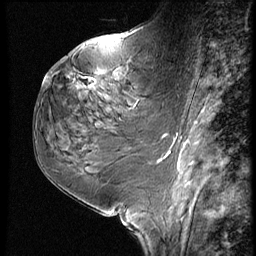
Breast MRI (dynamic contrast-enhanced), one sagittal slice. Position 30 of 60 along the scan axis. 3 images stored at this slice position (order not interpretable as contrast timing). 1.5 T. TE 4.2 ms, TR 9 ms. 256 × 256 image matrix, field of view 180 × 180 mm. Patient: female, 59 years. From the clinical record (not read from this slice): setting: breast cancer imaged before/during neoadjuvant chemotherapy; receptor status: HER2-positive.
Structures marked on this image (semi-automatically segmented with operator editing):
- analysis volume of interest (the breast-tissue region the enhancement analysis was run in; not a lesion): box from (x=78, y=61) to (x=161, y=125) px
- tumour enhancement mask (voxels above the 140 % enhancement threshold inside the analysis volume of interest): (x=82, y=78)–(x=94, y=87)